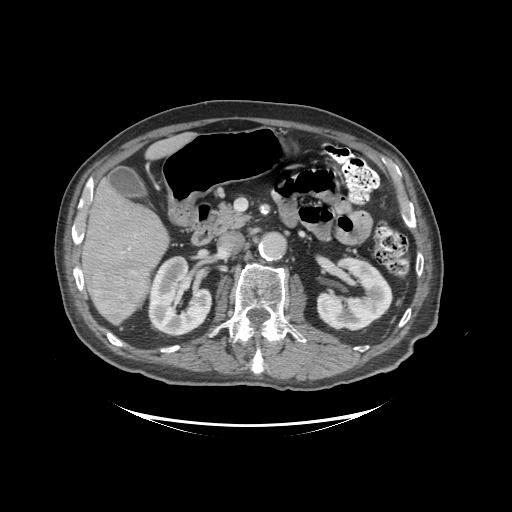
Contrast-enhanced abdominal CT (liver protocol), one axial slice. Slice 46 of 99 in the series (ordered by position). Reconstruction kernel STANDARD. Soft-tissue window (W 400 / L 40 HU). 512 × 512 image matrix, field of view 460 × 460 mm. Case-level facts recorded for this patient, not image findings: diagnosis: hepatocellular carcinoma (patient treated with transarterial chemoembolisation; whether this scan precedes or follows treatment is not stated here); TNM stage (as recorded): Stage-I; Child-Pugh class: A.
Structures marked on this image (semi-automatic segmentation, software-assisted and operator-edited):
- liver parenchyma outside the tumour (the mass and vessels are separate outlines, so this box may not span the whole liver): bounding box (x1, y1, x2, y2) in pixels: (82, 134, 190, 324)
- mass: (86, 260, 149, 318)